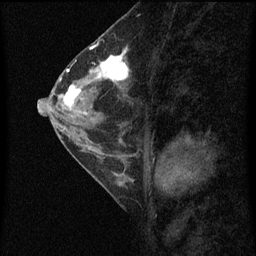
Breast MRI (dynamic contrast-enhanced), one sagittal slice; slice 31 of 60 in the series (ordered by position); dynamic contrast-enhanced series, image 2 of 4 at this slice position (ordered by acquisition); 1.5 T; TE 4.2 ms, TR 8 ms; 2 mm slice thickness; 256 × 256 image matrix. Patient: female, 56 years.
Structures marked on this image (semi-automatic segmentation, software-assisted and operator-edited):
- analysis volume of interest (the breast-tissue region the enhancement analysis was run in; not a lesion): bounding box [x1, y1, x2, y2] px = [56, 52, 132, 115]
- tumour enhancement mask (voxels above the 70 % enhancement threshold inside the analysis volume of interest): [59, 52, 130, 107]